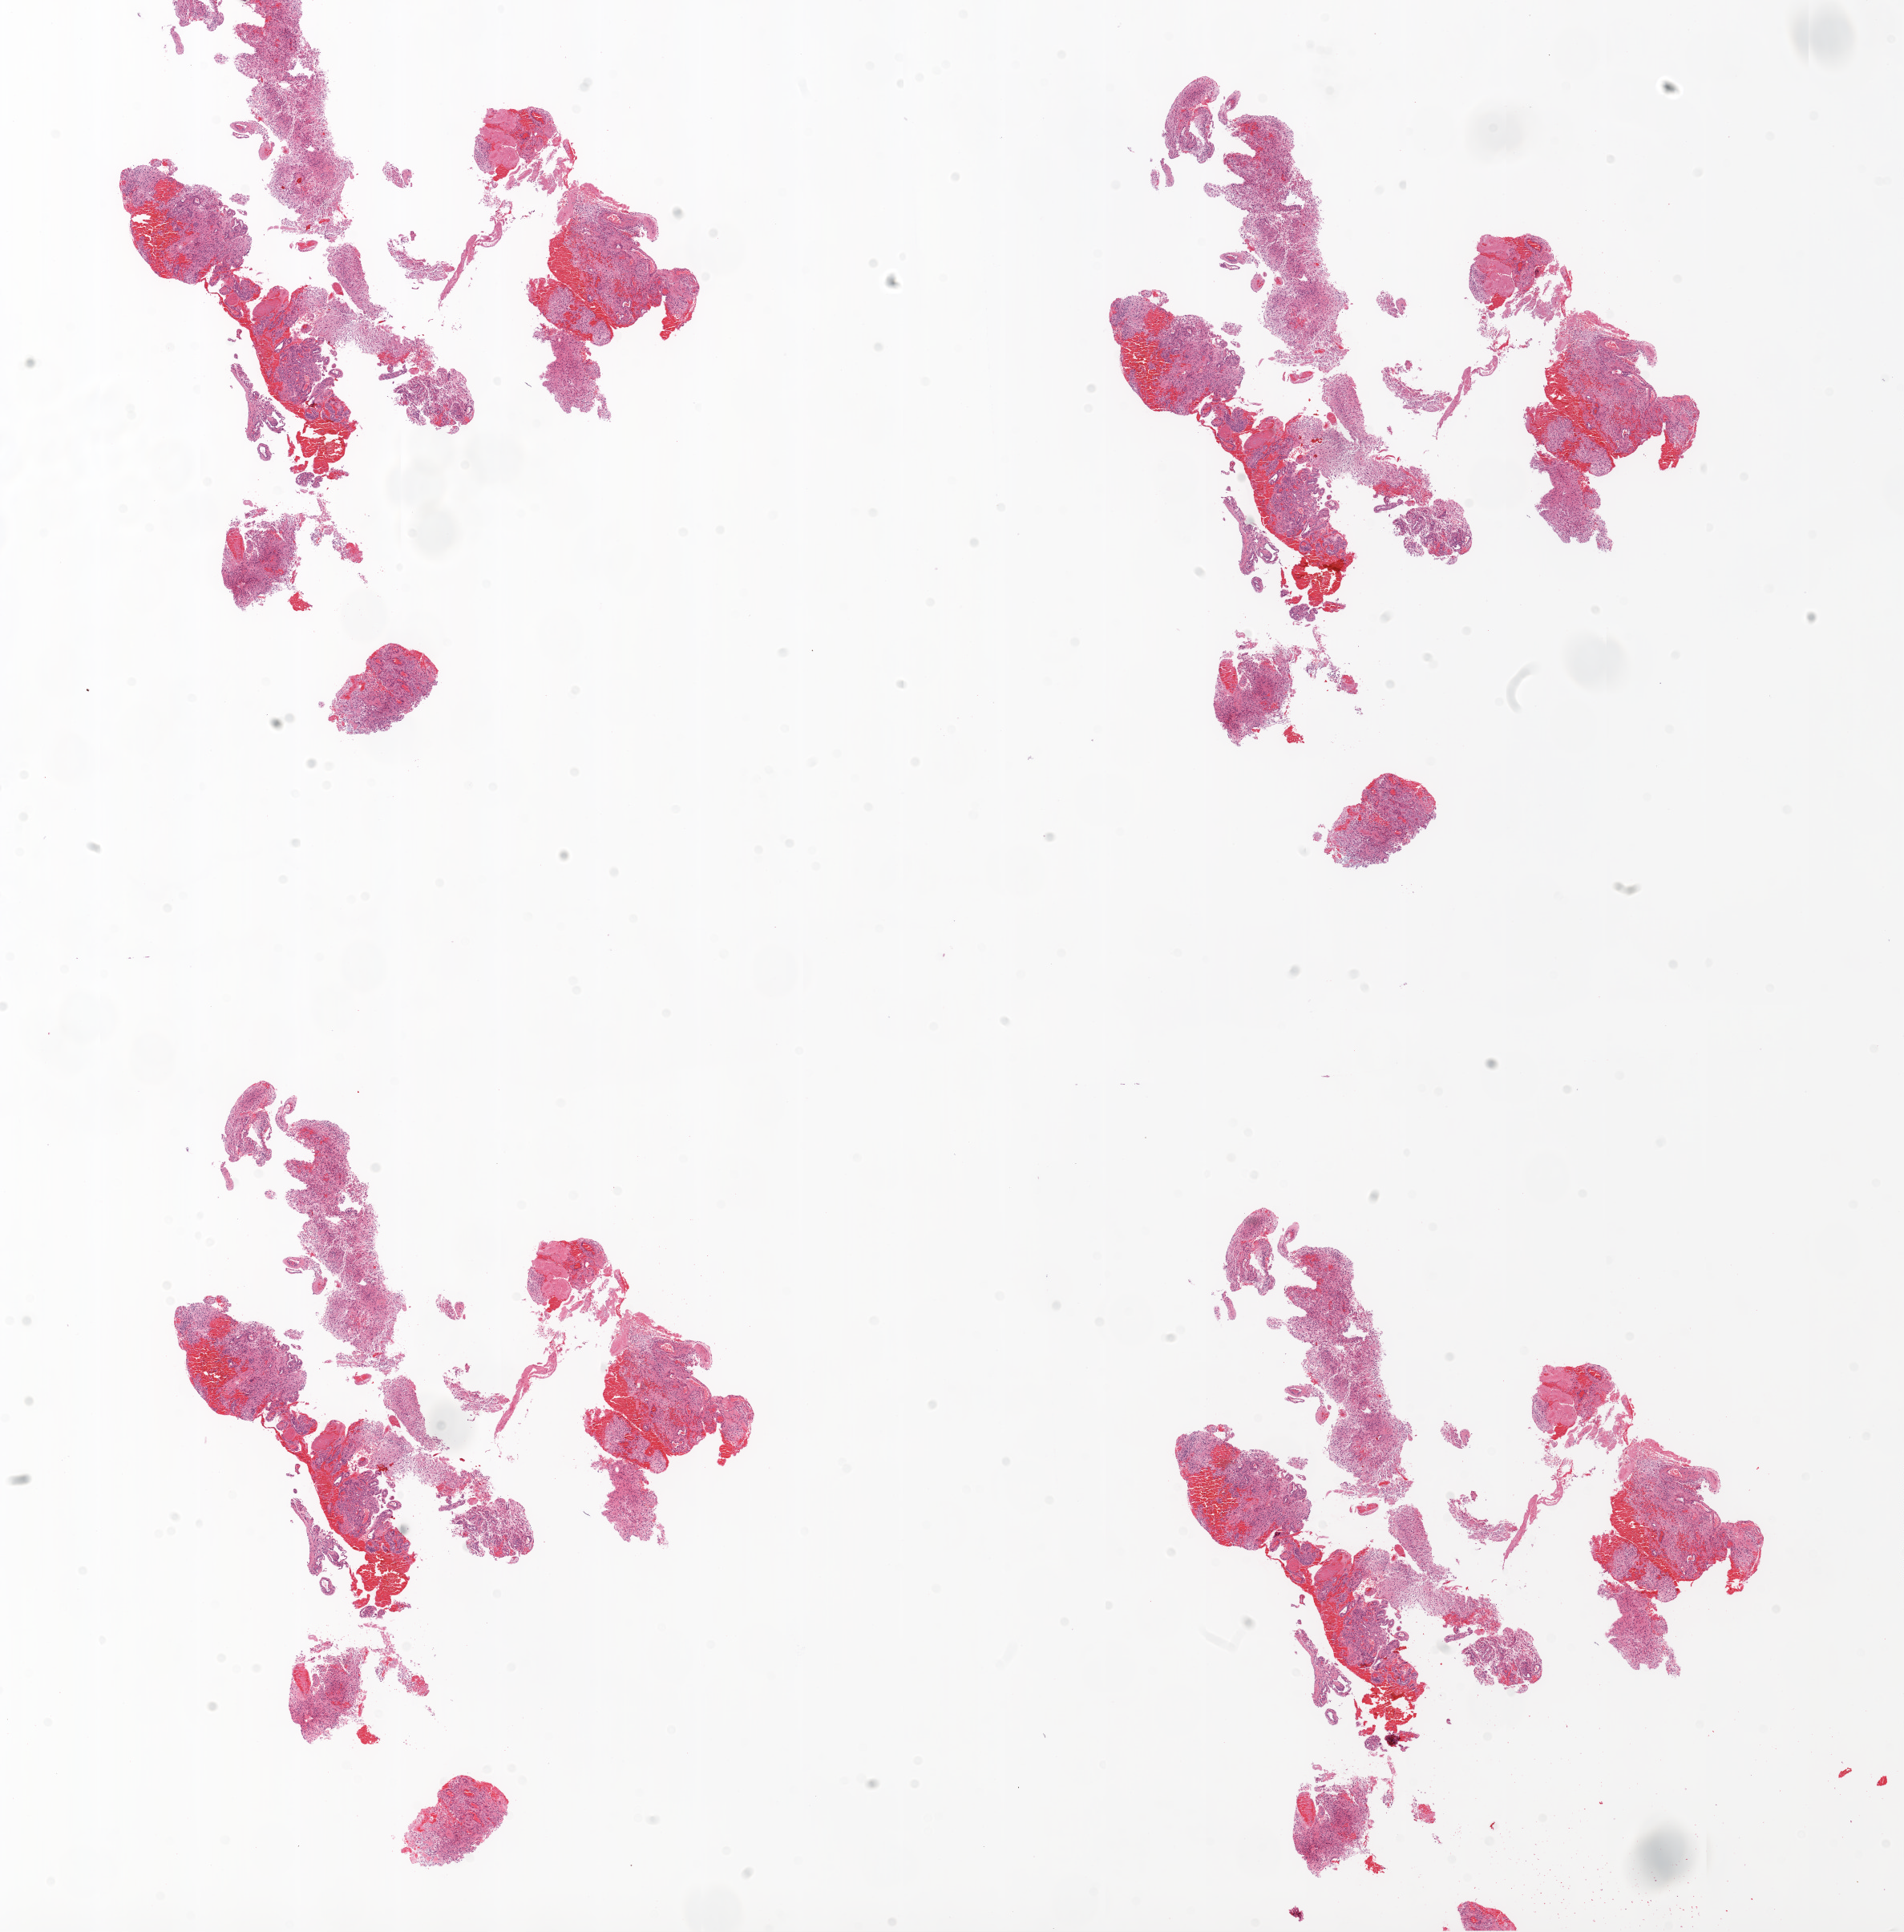
Digitized Hematoxylin and eosin (H&E) stained tissue section (whole slide) — whole scanned area (about 19.1 x 19.3 mm, slide scanned at 20x) shown as a low-resolution overview; formalin-fixed paraffin-embedded (FFPE) diagnostic section; sample: primary tumour, brain. Patient: male, age at initial diagnosis 43 years.
* histologic diagnosis: Glioblastoma